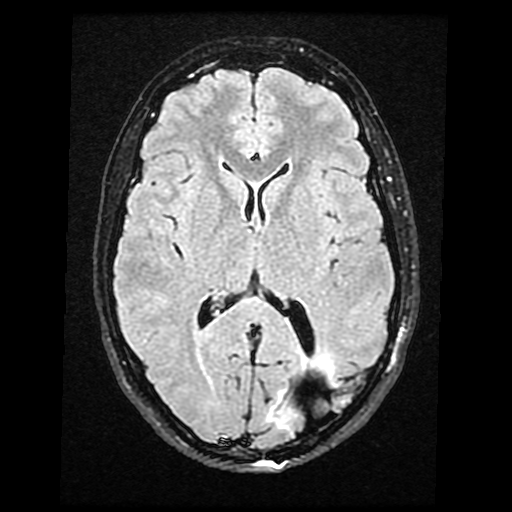
Brain MRI from a brain-tumour surgery series, one axial slice; position 20 of 40 along the scan axis; T2 FLAIR; 4 mm slice thickness; 512 × 512 image matrix. Case-level facts recorded for this patient, not image findings: histopathology: Glioma with ependymal features; WHO grade: 2.
Annotated regions visible in this slice (expert manual segmentation):
- tumour: box from (x=265, y=355) to (x=340, y=434) px